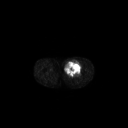
FDG PET of an extremity soft-tissue mass (from a PET/CT study), one axial slice; slice 243 of 267 in the series (ordered by position); 3.27 mm slice thickness; 128 × 128 image matrix, field of view 700 × 700 mm. Male patient, age 63 years. From the clinical record (not read from this slice): histological type: pleiomorphic liposarcoma; grade: high; site of the primary tumour: left thigh.
Outlined on this slice (expert contour drawn on MRI and transferred to this co-registered scan by the dataset authors):
- gross tumour volume including surrounding oedema: bounding box <65,60,82,76> (left, top, right, bottom; pixels)
- gross tumour volume (mass): <65,60,82,76>